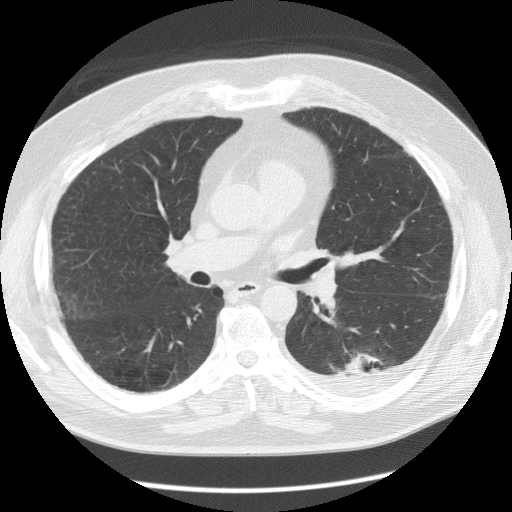
Low-dose screening chest CT, axial slice. First (baseline) screen. Lung window (W 1500 / L -600 HU). 2.5 mm slice thickness. Standard (soft-tissue) reconstruction kernel (STANDARD). Slice 55 of 126 in the series. 512 × 512 image matrix. Male participant, aged 56 years at enrolment. Former smoker at enrolment.
Expert-annotated lung lesion, box from (x=323, y=339) to (x=395, y=392) px. The screening reader recorded 4 non-calcified nodules or masses ≥4 mm on this exam (left lower lobe, left lower lobe, right middle lobe, left upper lobe); which of them this box marks is not recorded. Official screen result: positive, change unspecified: nodule(s) >= 4 mm or enlarging nodule(s), mass(es), or other non-specific abnormalities suspicious for lung cancer. Participant outcome: lung cancer diagnosed 173 days after this screen — non-small cell carcinoma, left lower lobe, stage IV (AJCC 6th edition), 50 mm at pathology.